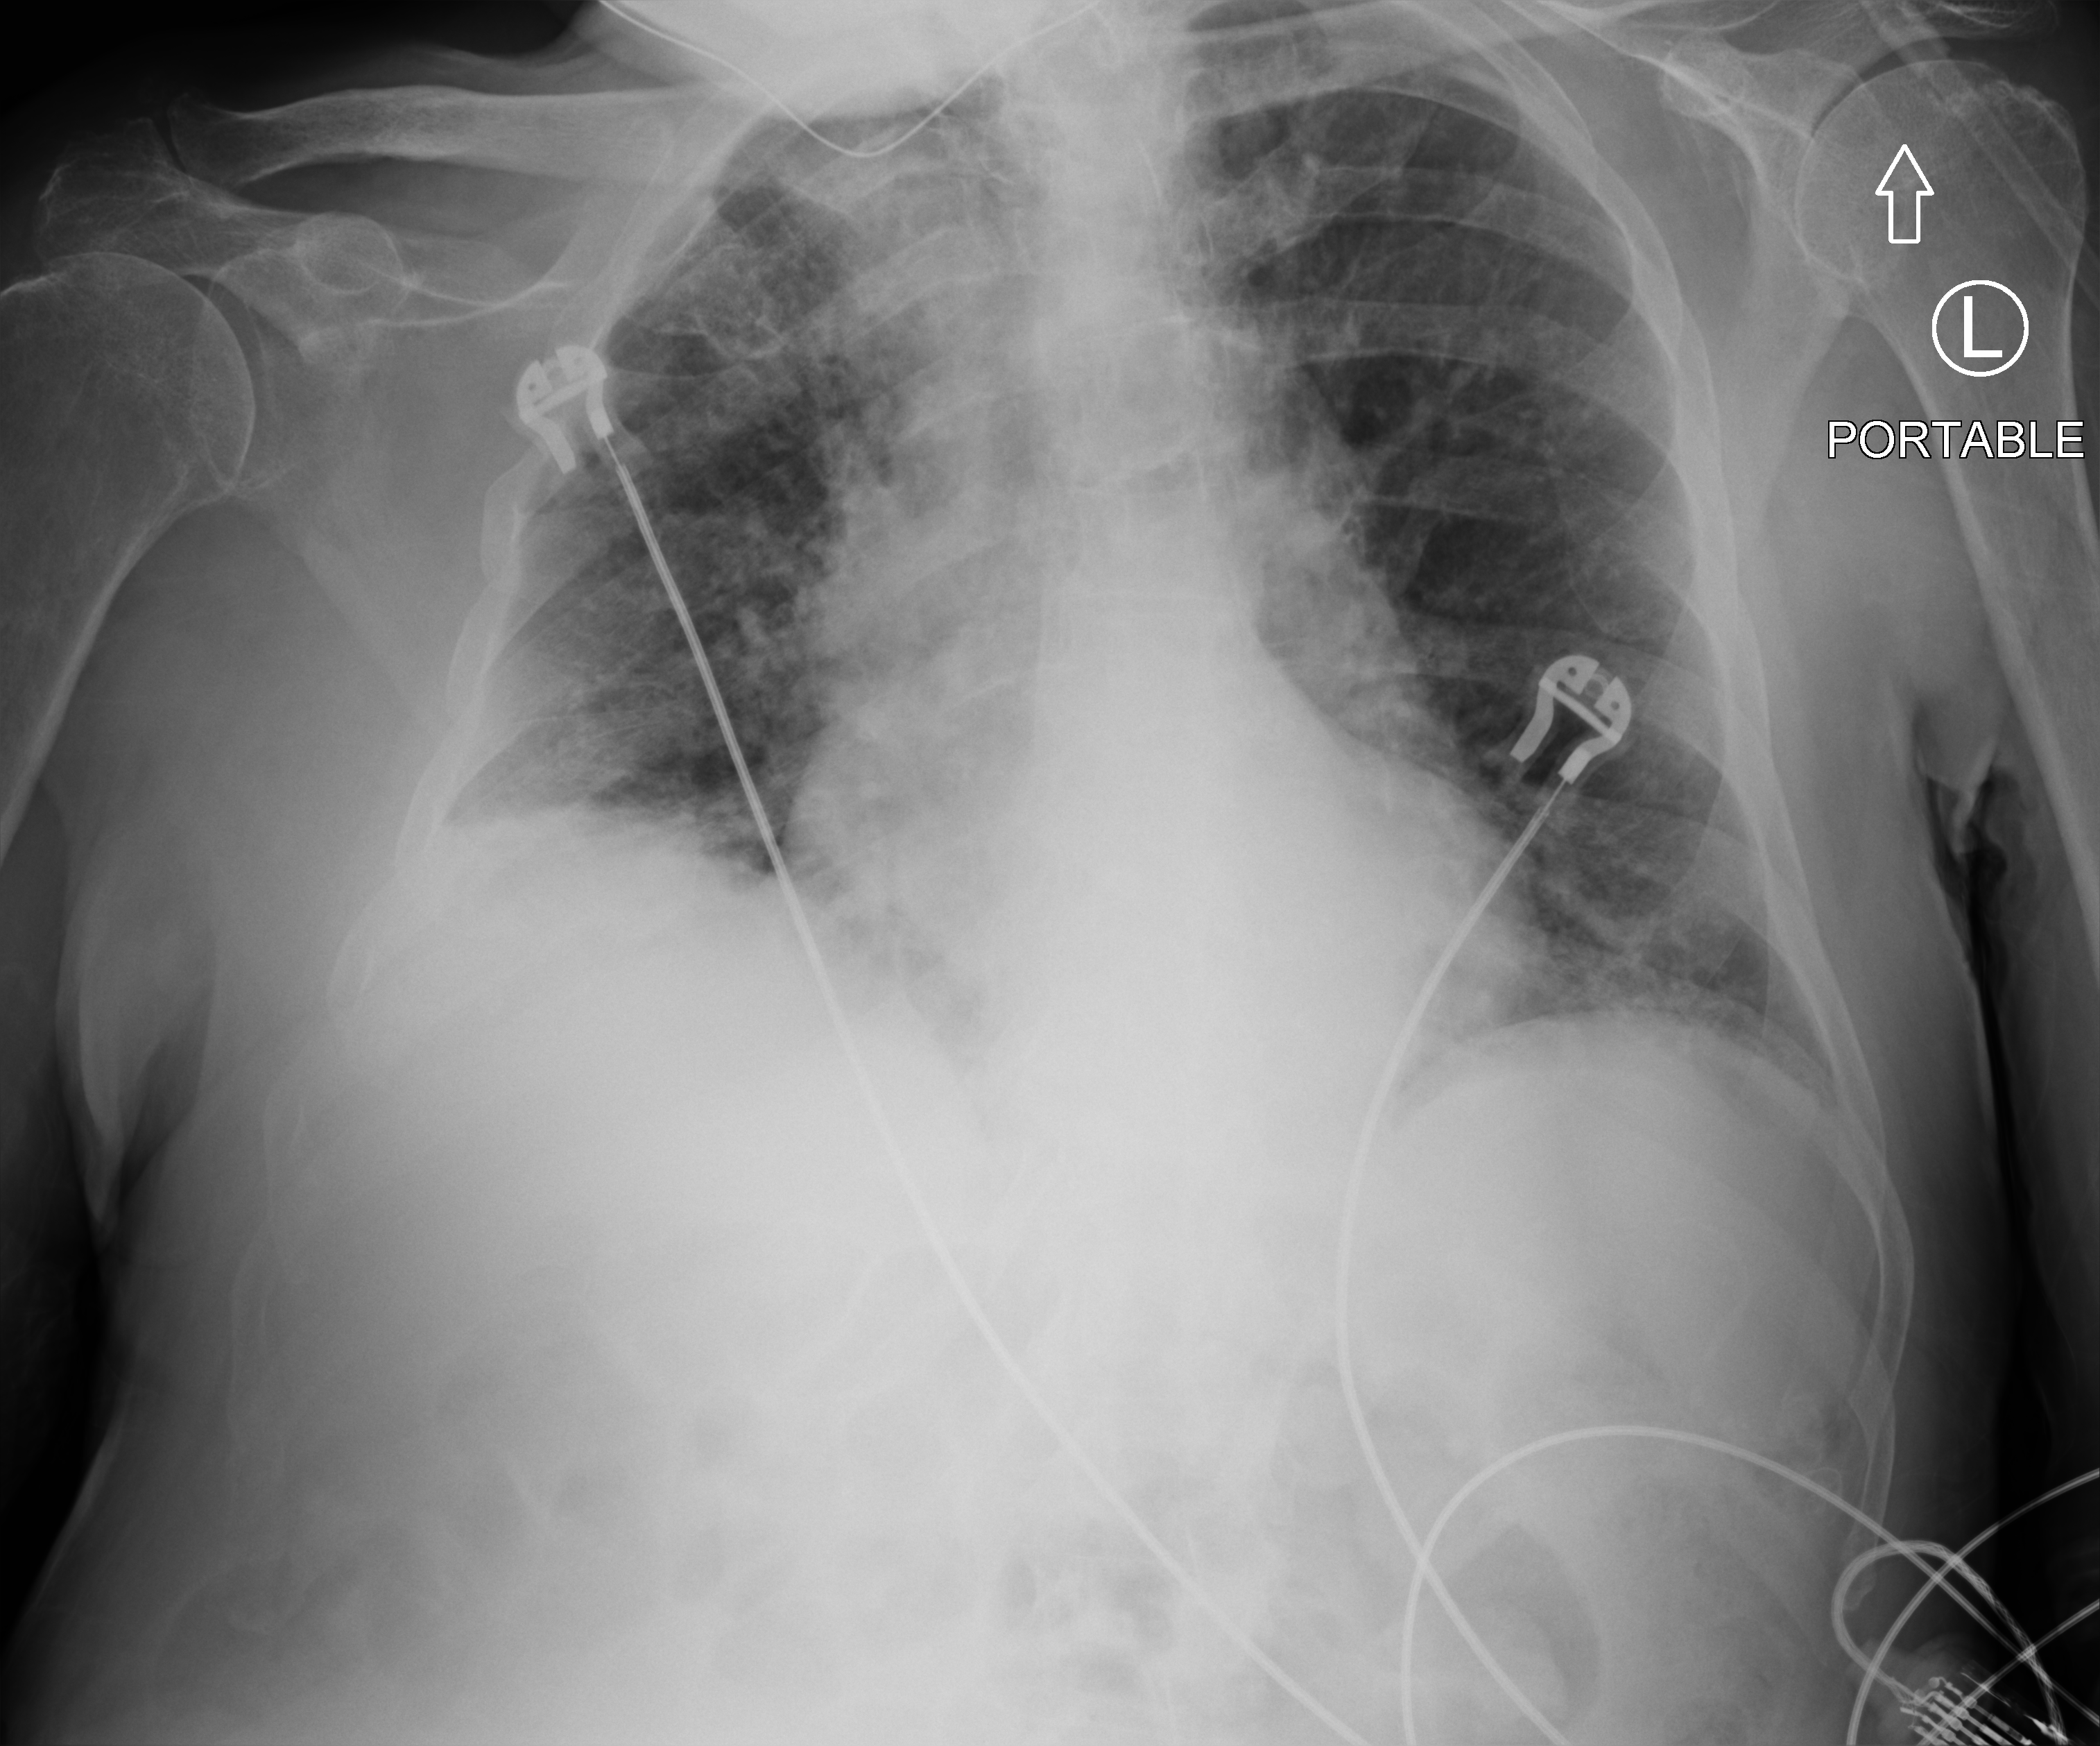
Bedside chest radiograph (computed radiography); anteroposterior (AP) projection. Patient hospitalised with COVID-19; male, aged 75–90 years.
From the hospital-stay record, not from the radiograph (when in the stay this image was taken is not recorded):
- admitted to intensive care during this hospital stay: yes
- chronic kidney disease (admission record): no